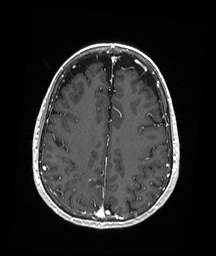
Brain MRI from a brain-tumour surgery series, one axial slice; T1-weighted post-contrast; 1 mm slice thickness; 216 × 256 image matrix, field of view 211 × 250 mm. Case-level facts recorded for this patient, not image findings: histopathology: Astrocytoma; WHO grade: 3; IDH mutation: yes.
Annotated regions visible in this slice (expert manual segmentation):
- tumour: bounding box (x1, y1, x2, y2) in pixels: (89, 178, 96, 181)